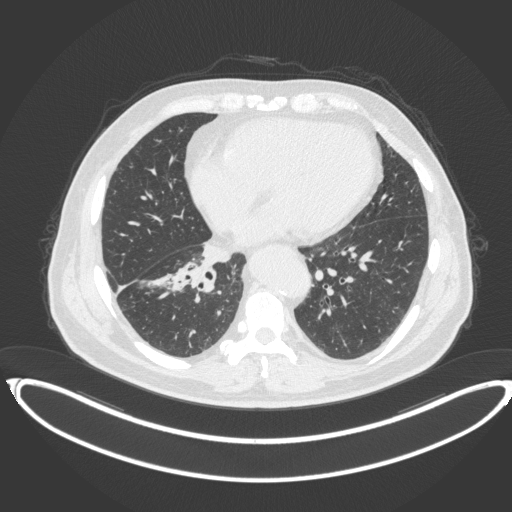
Chest CT, one axial slice; position 157 of 383 along the scan axis; reconstruction kernel B31f; 120 kVp; lung window (W 1500 / L -600 HU); 1 mm slice thickness; 512 × 512 image matrix, field of view 448 × 448 mm. Patient: male, 61 years. From the clinical record (not read from this slice): clinical TNM (as recorded): T1b N1 M0.
Outlined on this slice (rectangle marked by the reading radiologist):
- lung tumour (recorded histology: squamous cell carcinoma): bounding box <169,258,218,297> (left, top, right, bottom; pixels)